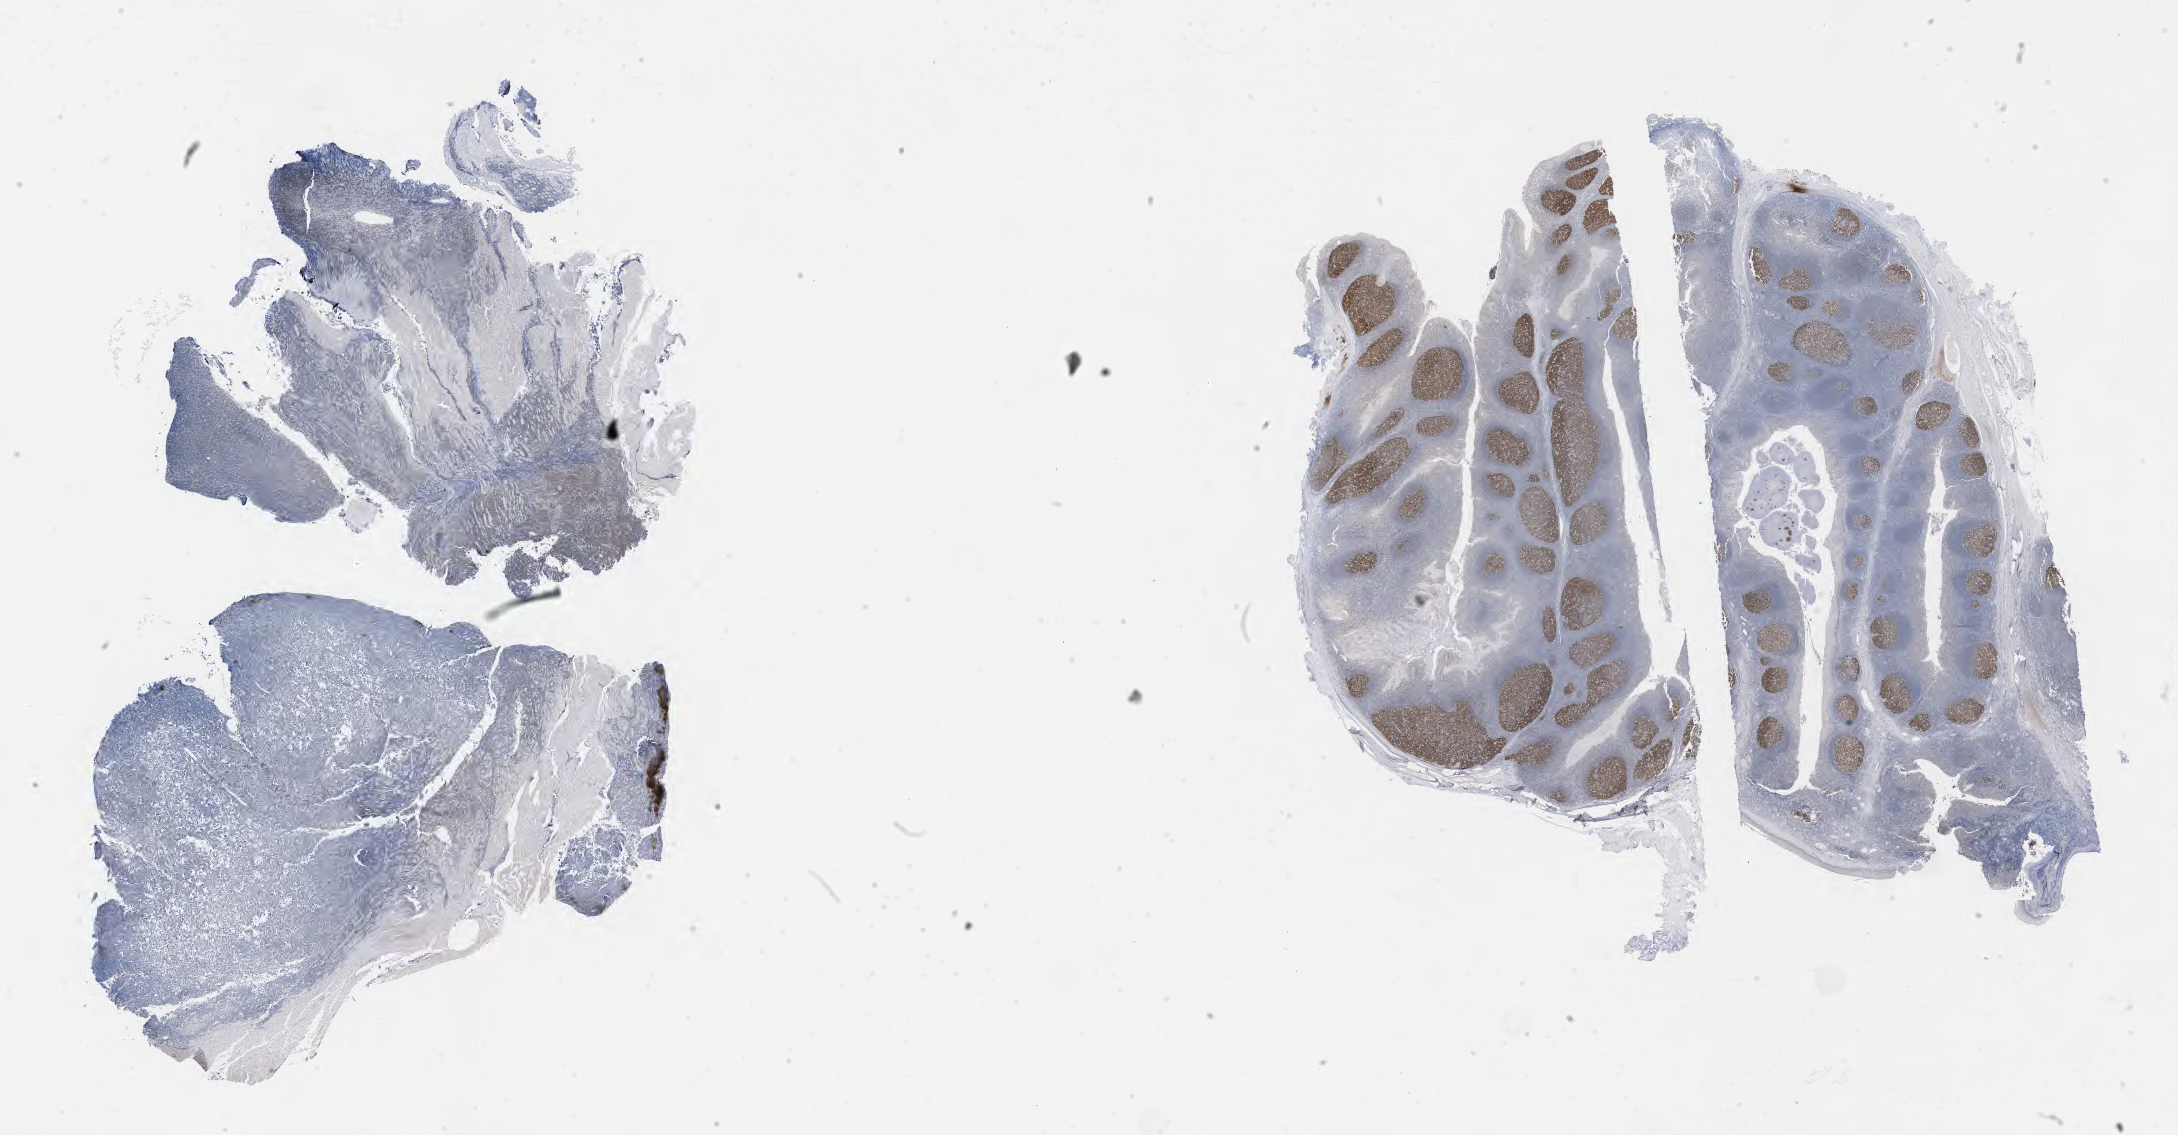
Immunohistochemistry (IHC) whole-slide image stained for BCL6, whole scanned area (about 35.2 x 18.3 mm) shown as a low-resolution overview; tumor tissue. Patient male; age 40 years.
Histologic diagnosis: Burkitt lymphoma, NOS.